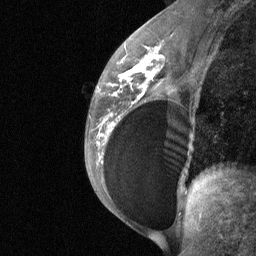
Breast MRI (dynamic contrast-enhanced), one sagittal slice. Position 36 of 64 along the scan axis. Dynamic contrast-enhanced study with each time point stored as its own series, time point 2 of 3 at this slice position (early post-contrast, ordered by acquisition time). 1.5 T. TE 4.8 ms, TR 27 ms. 2 mm slice thickness. 256 × 256 image matrix. Patient: female, 34 years. Case-level facts recorded for this patient, not image findings: setting: breast cancer imaged before/during neoadjuvant chemotherapy; receptor status: HR-positive, HER2-negative.
Annotated regions visible in this slice (semi-automatic segmentation, software-assisted and operator-edited):
- analysis volume of interest (the breast-tissue region the enhancement analysis was run in; not a lesion): bounding box (x1, y1, x2, y2) in pixels: (92, 50, 188, 185)
- tumour enhancement mask (voxels above the 90 % enhancement threshold inside the analysis volume of interest): (108, 55, 162, 127)